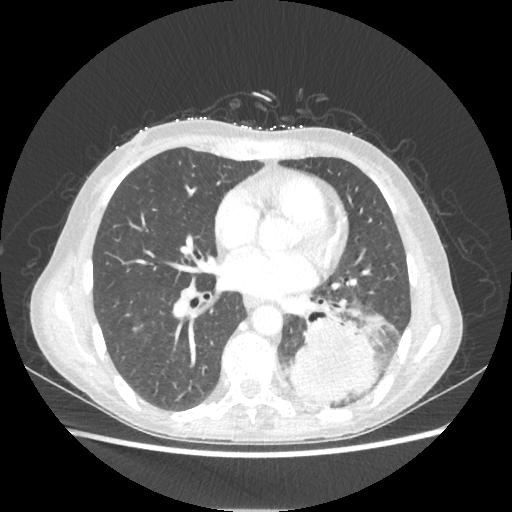
Chest CT, one axial slice. Position 100 of 221 along the scan axis. 80 kVp. Lung window (W 1500 / L -600 HU). 512 × 512 image matrix, field of view 360 × 360 mm. Patient: female, 53 years. Case-level facts recorded for this patient, not image findings: clinical TNM (as recorded): T3 N0 M0.
Structures marked on this image (rectangle marked by the reading radiologist):
- lung tumour (recorded histology: adenocarcinoma): box from (x=285, y=316) to (x=378, y=403) px